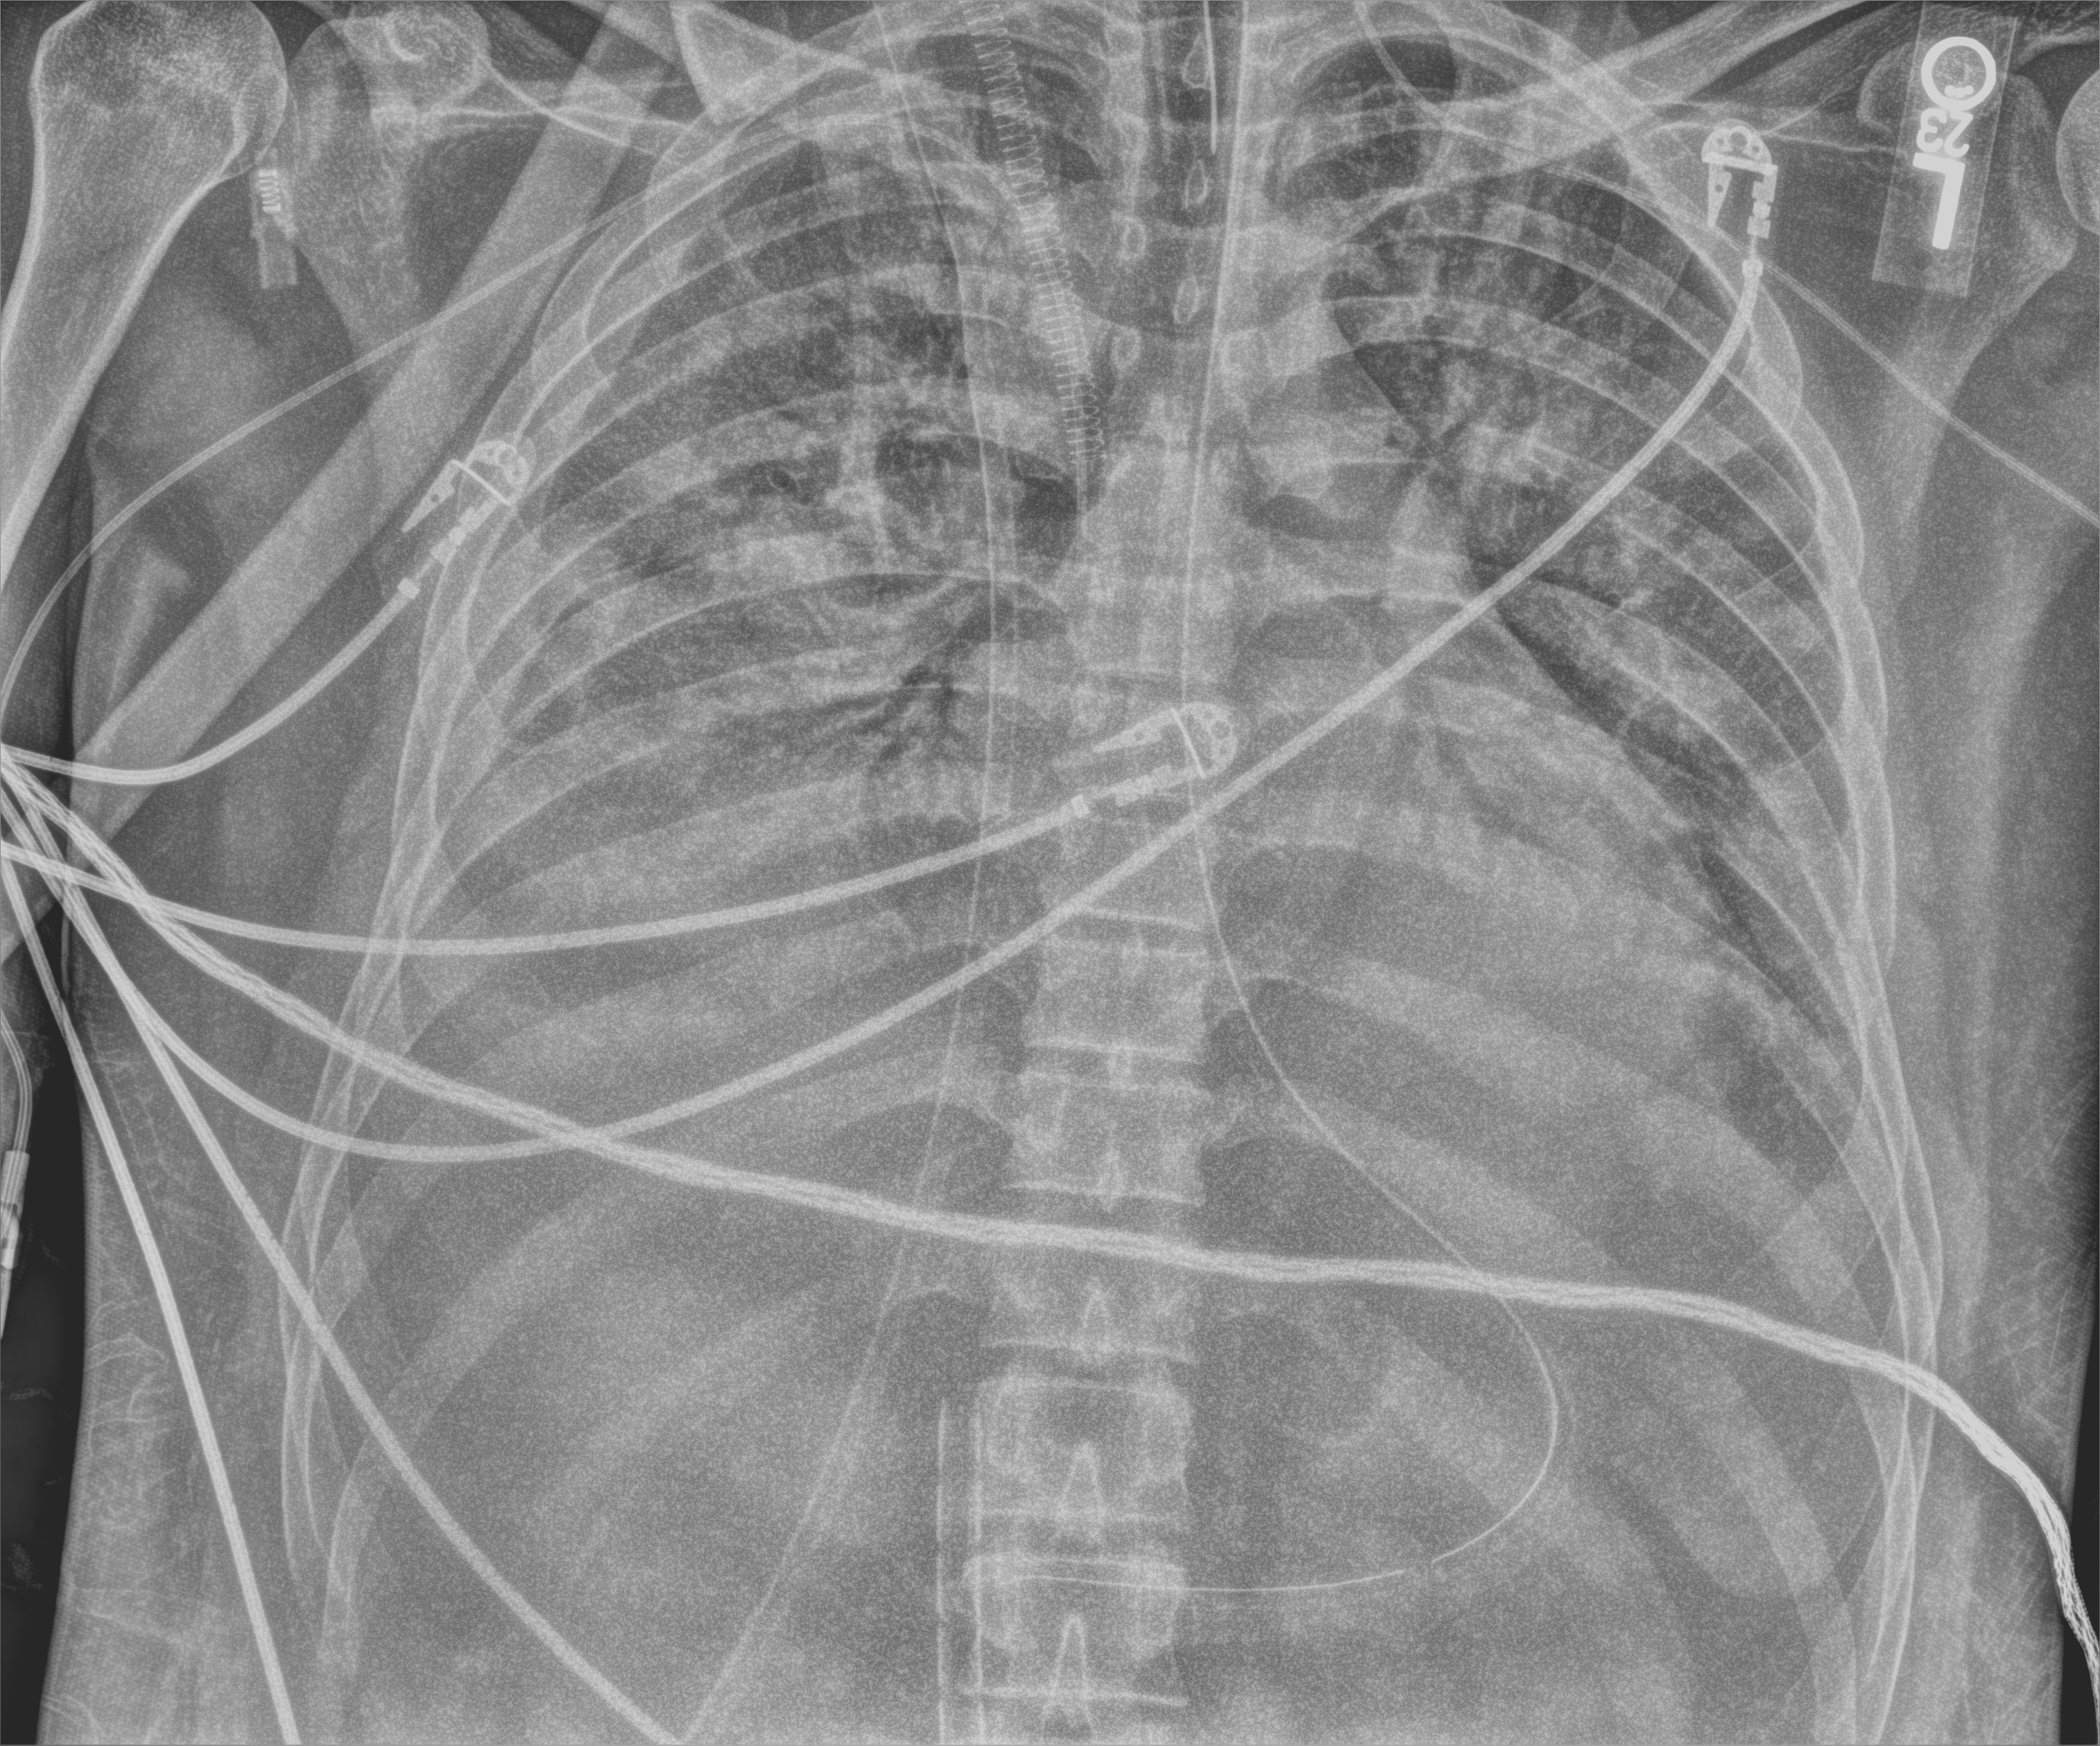
Portable chest radiograph; anteroposterior (AP) projection. Adult patient hospitalised with COVID-19, age 18–59 years.
Hospital-stay facts (about this admission, not read from this image; timing relative to this image not recorded): chronic kidney disease (admission record): no.